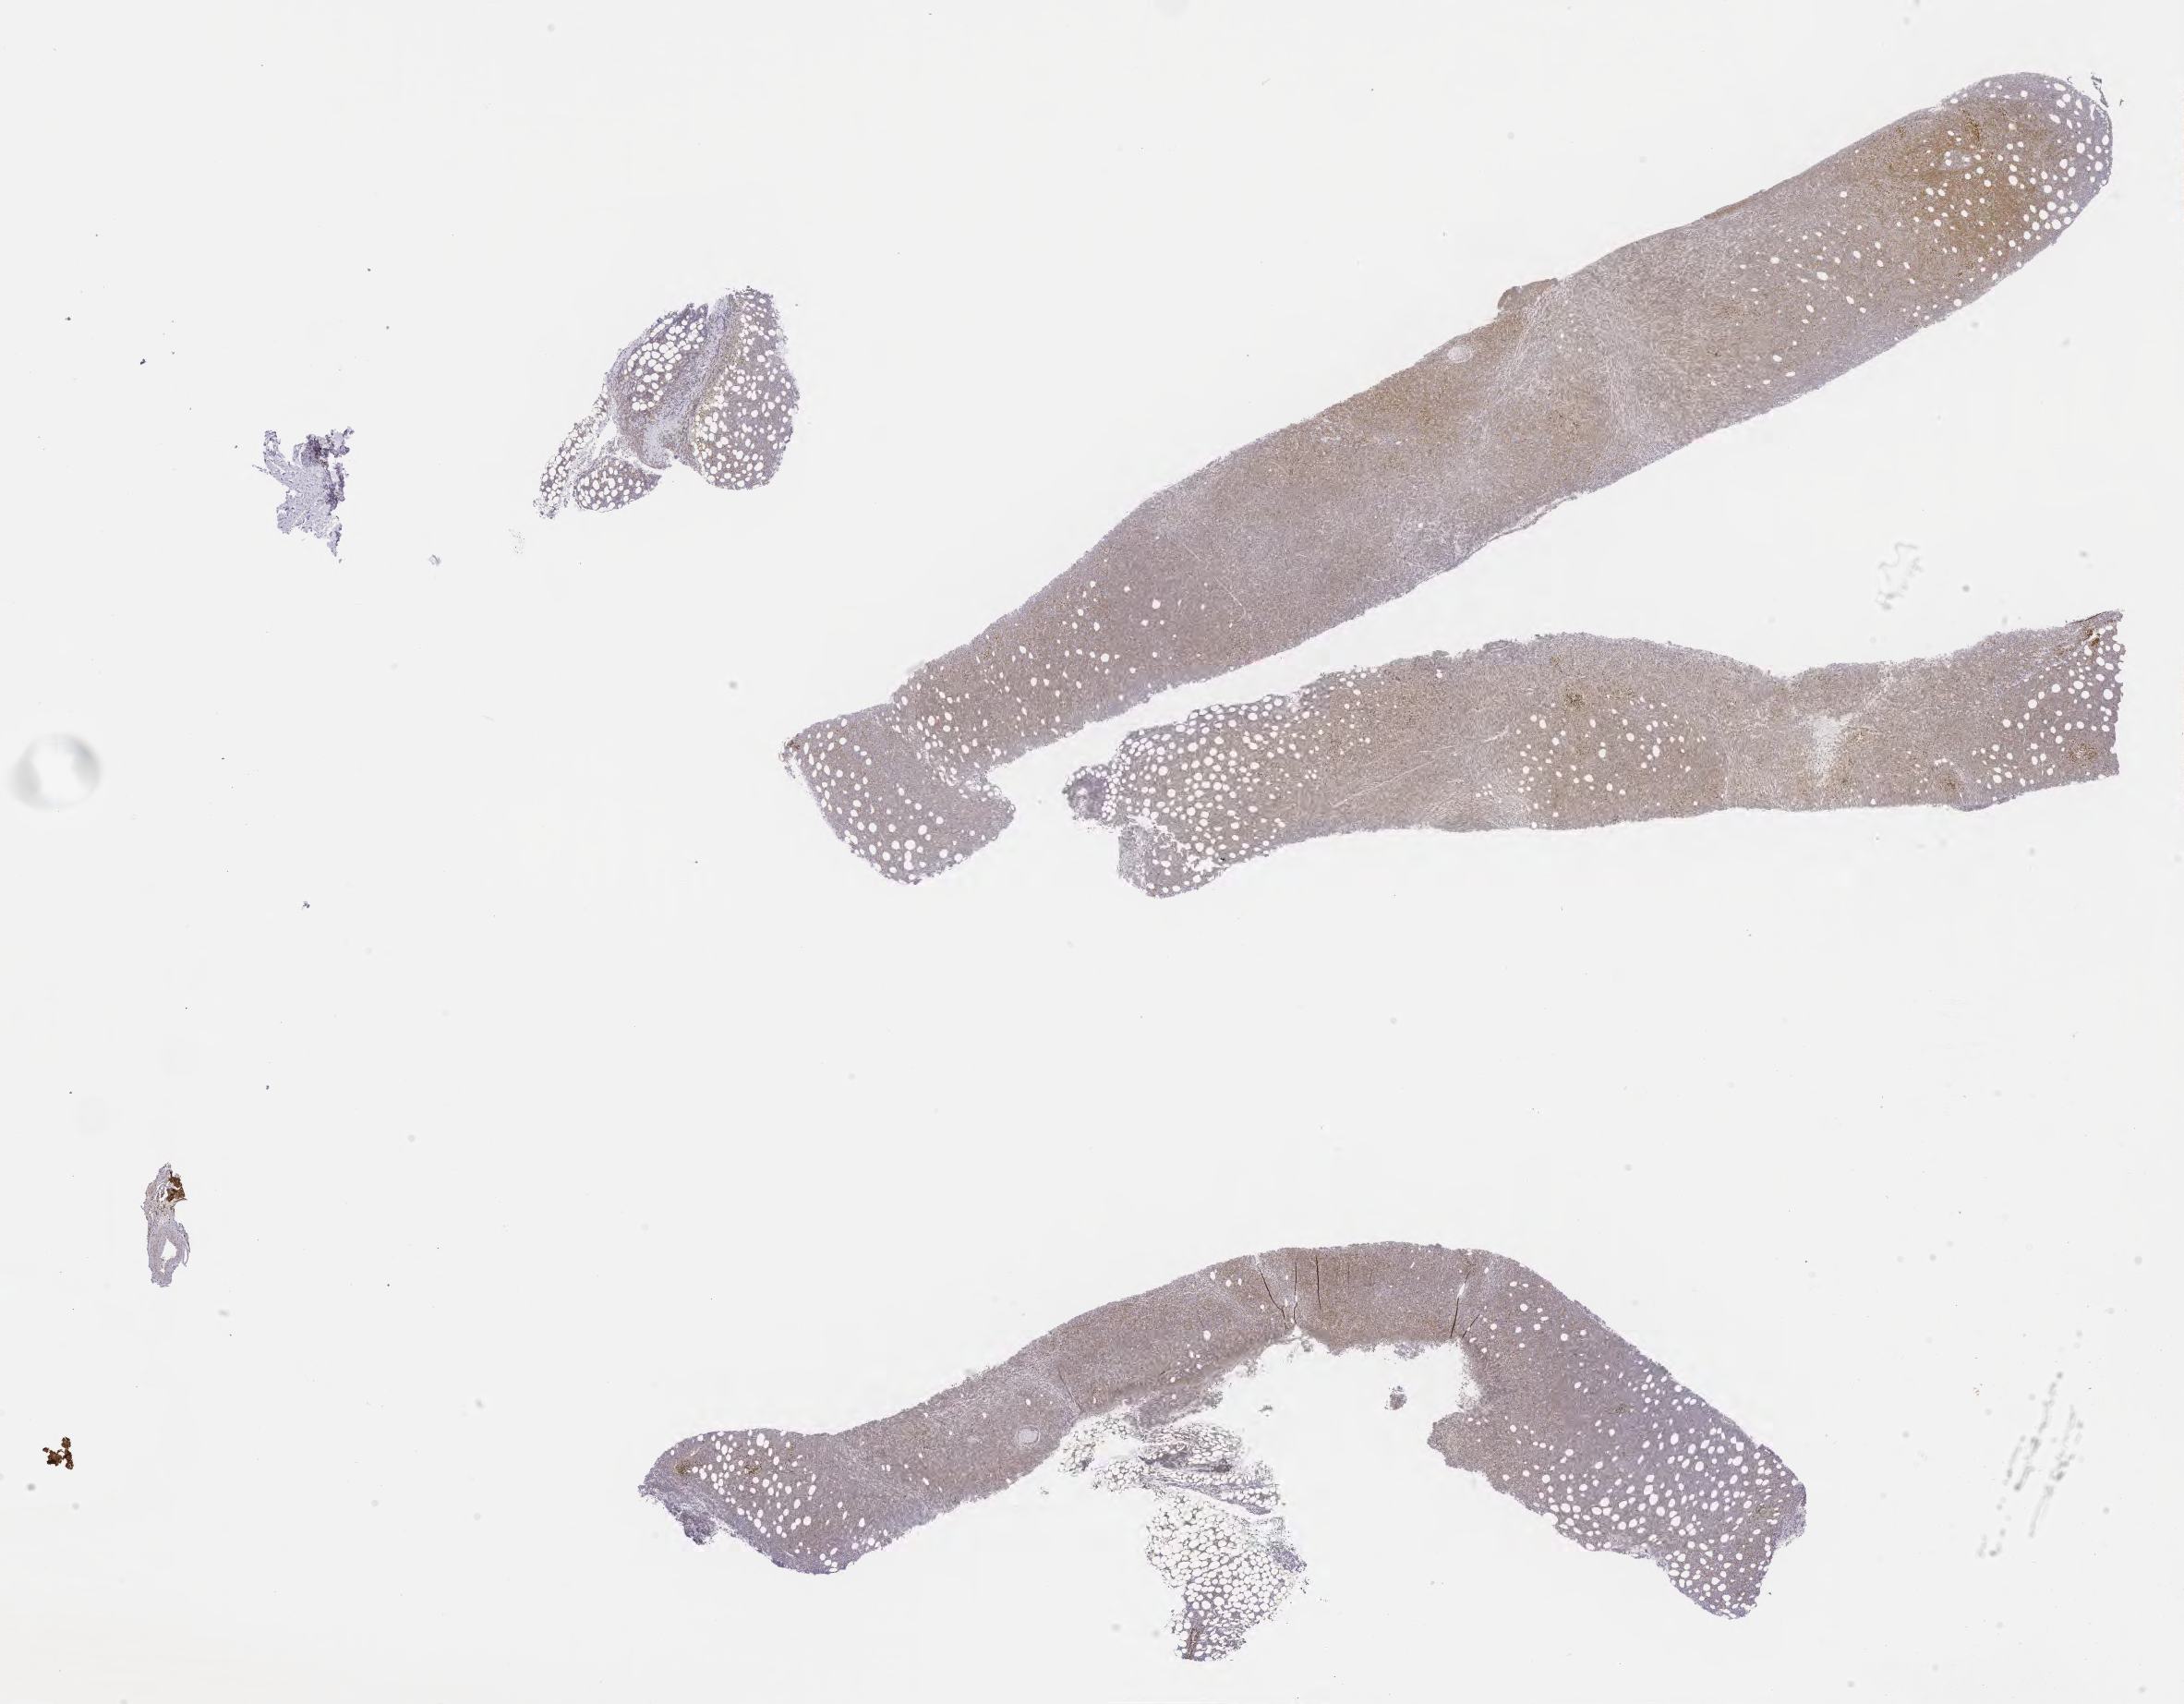
Whole-slide image, immunohistochemical stain for BCL2, shown as a low-resolution overview of the whole scanned area (about 19.1 x 14.9 mm), tumor tissue. Patient female; age 43 years.
* histologic diagnosis: Burkitt lymphoma, NOS